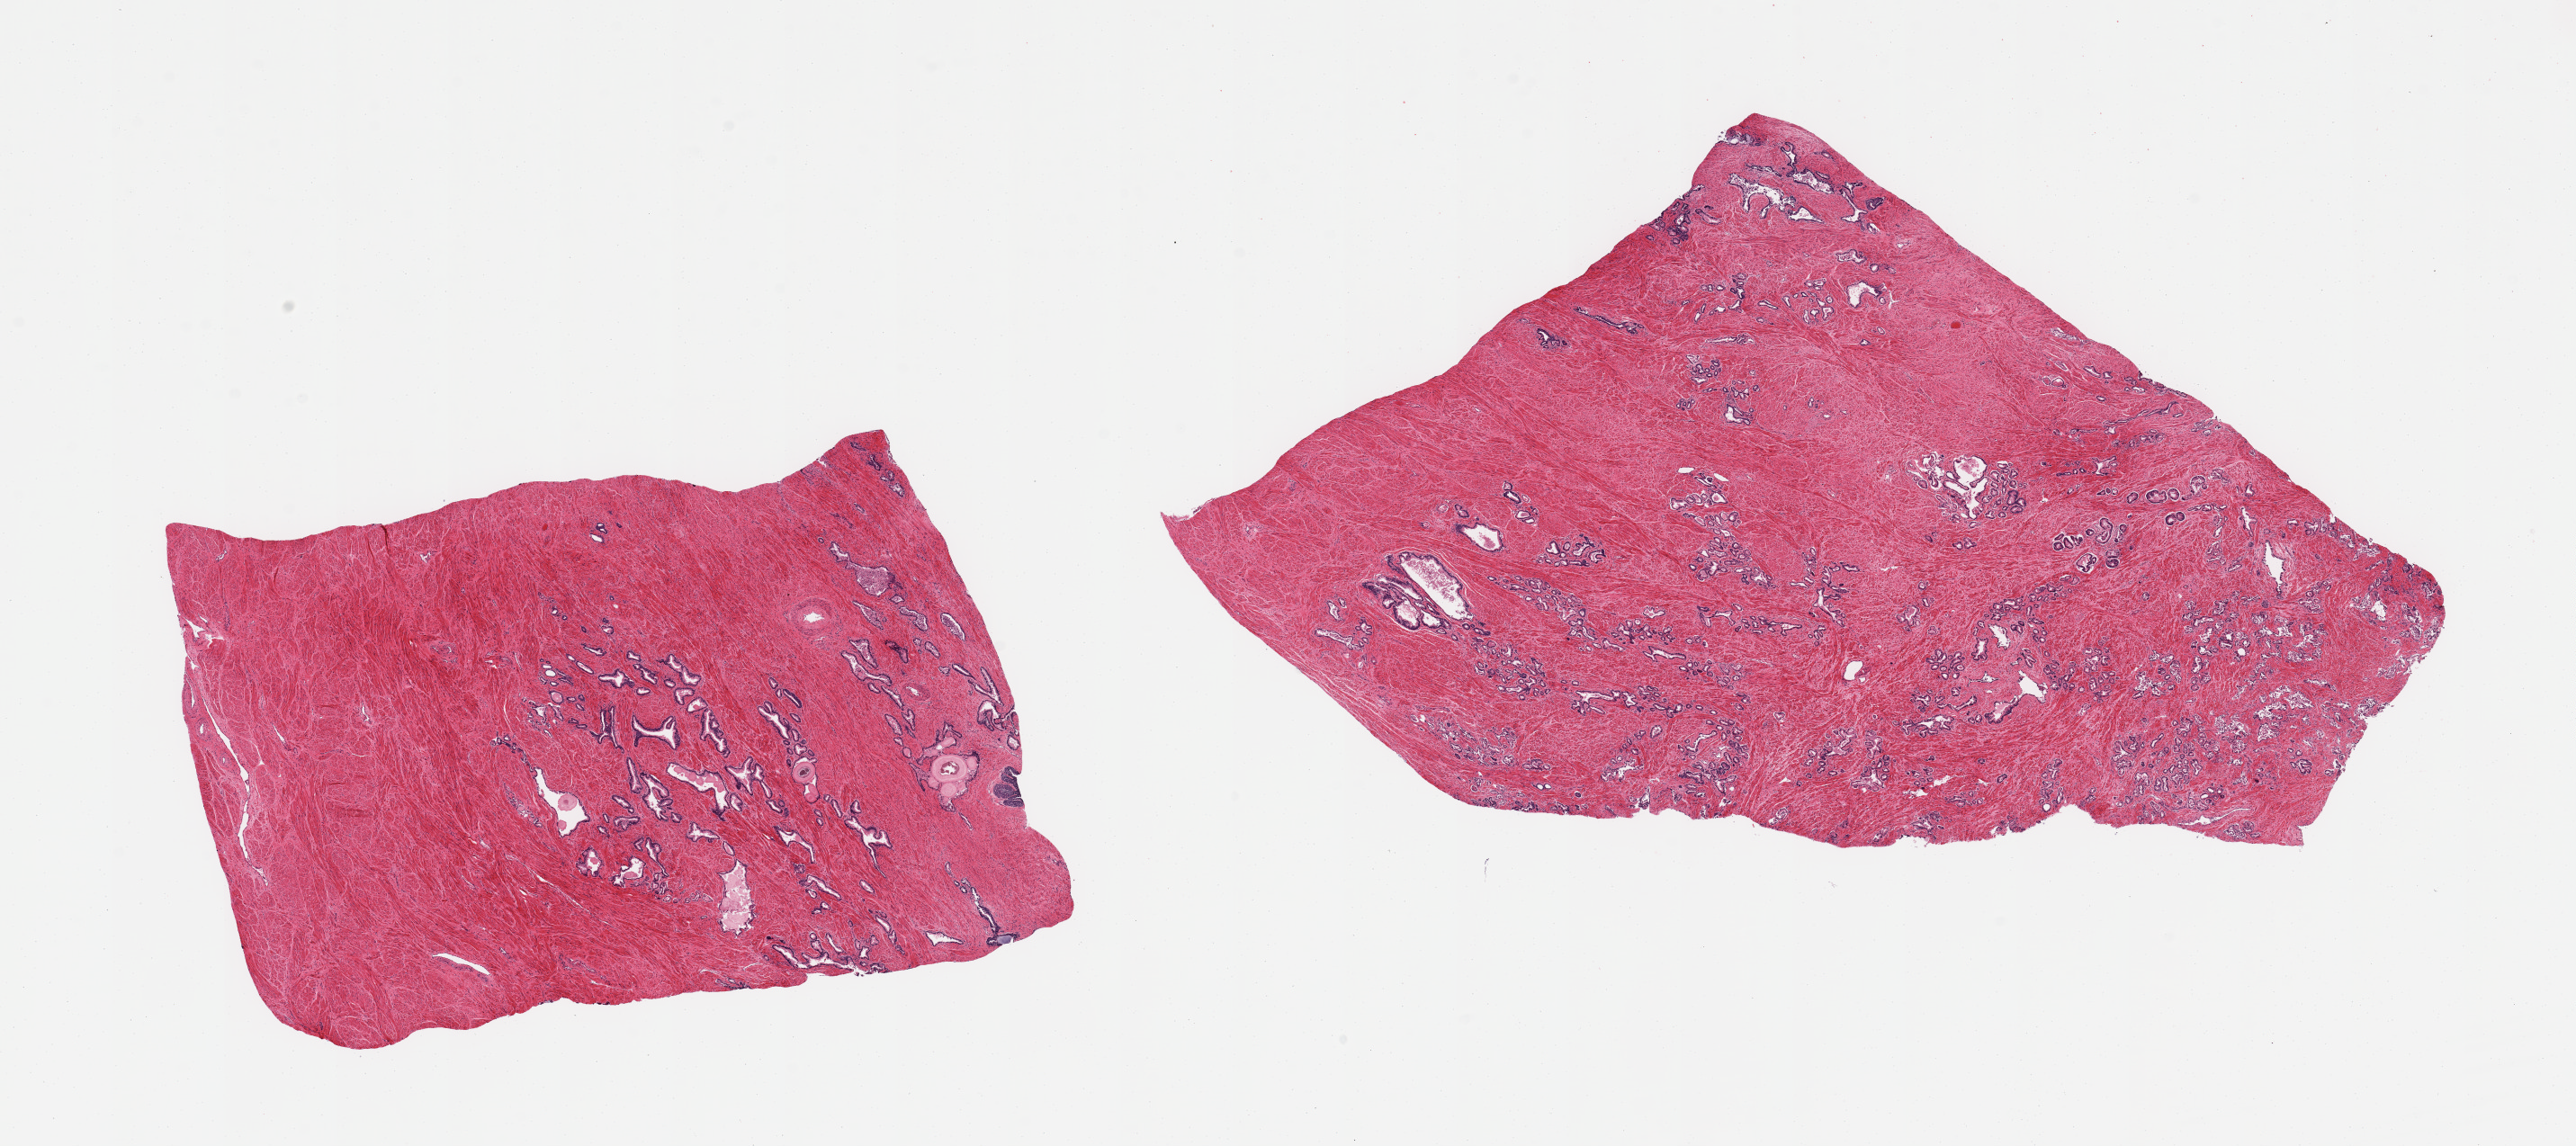
Whole-slide image, hematoxylin and eosin (H&E) stain, whole scanned area (about 22.6 x 10.1 mm, acquisition: 20x scan) shown as a low-resolution overview. PAXgene-fixed, paraffin-embedded tissue. Target tissue: prostate. Donor tissue sample. Donor sex: male.
Review note (as recorded): 2 pieces; more stroma than glands.